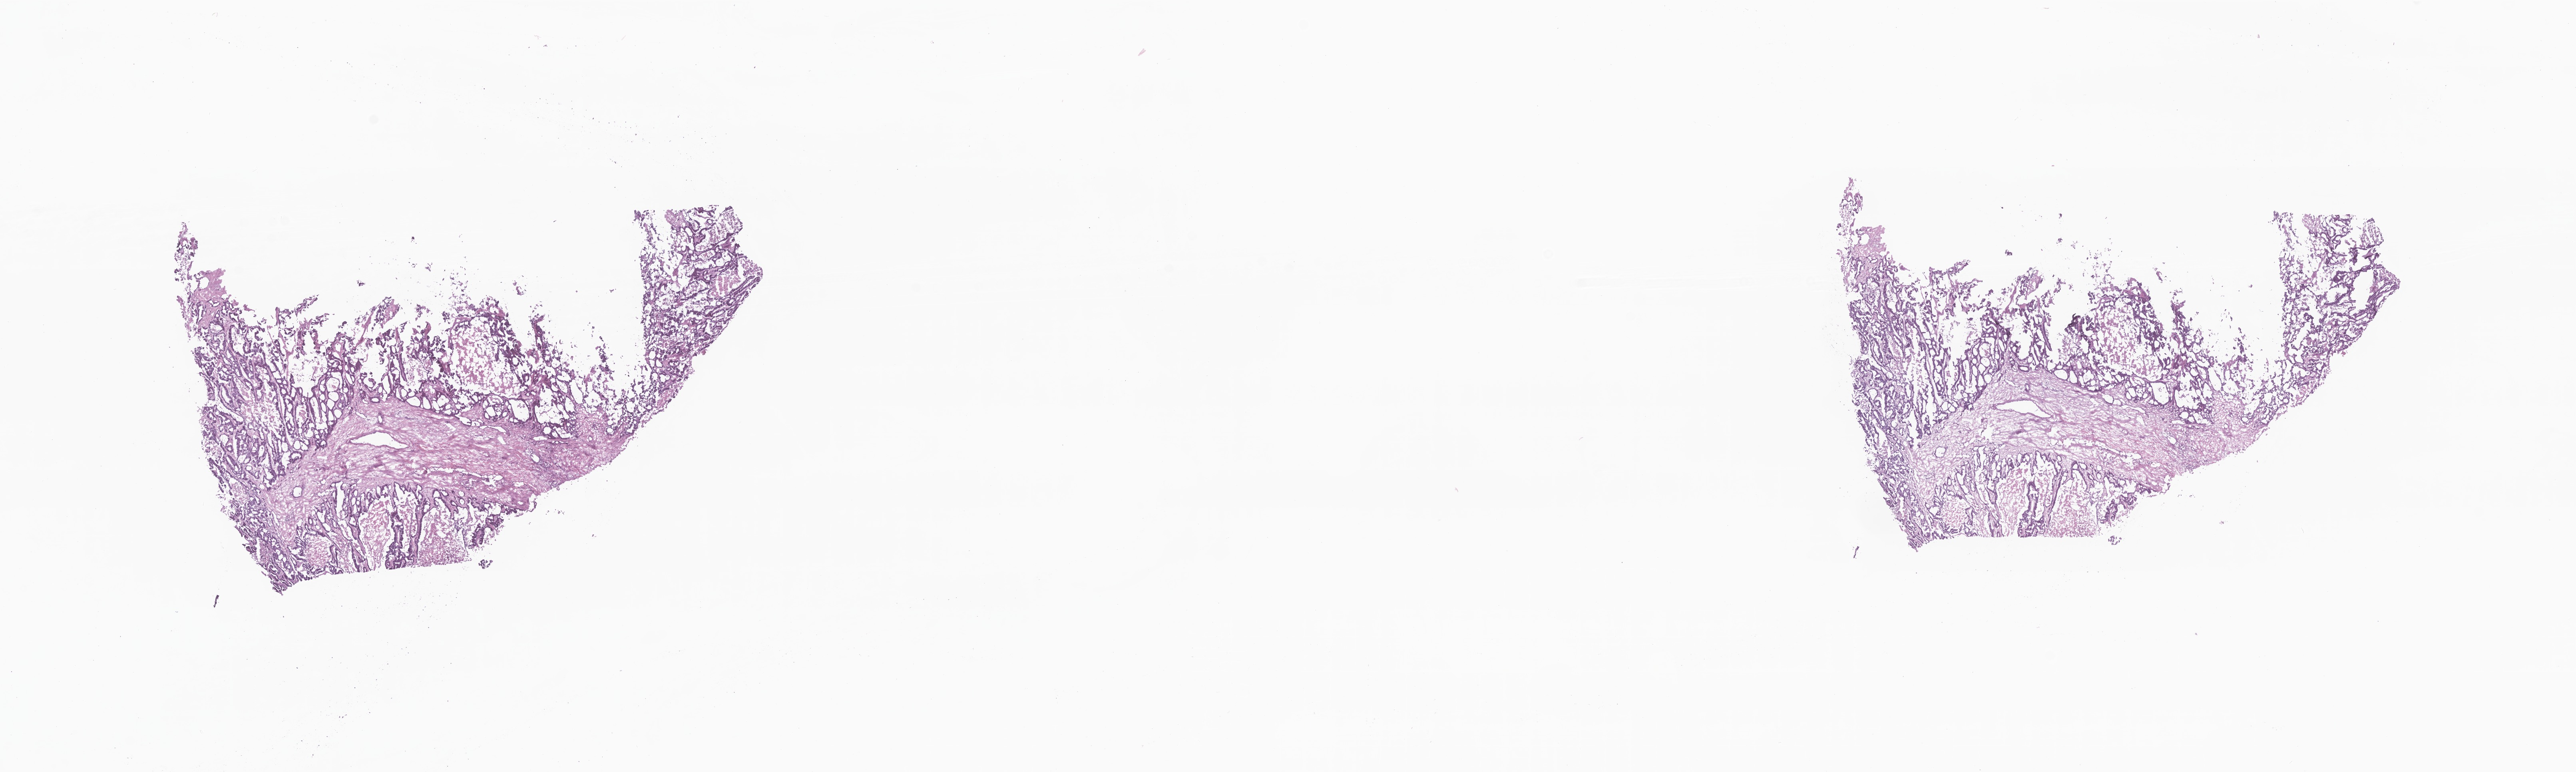
Digitized haematoxylin and eosin-stained section — whole scanned area (about 27.2 x 8.1 mm) shown as a low-resolution overview. Cryosection. Metastatic tumor tissue, resected from liver. Patient: male, age at initial diagnosis 71 years.
Patient diagnosis (primary): Adenocarcinoma, NOS.